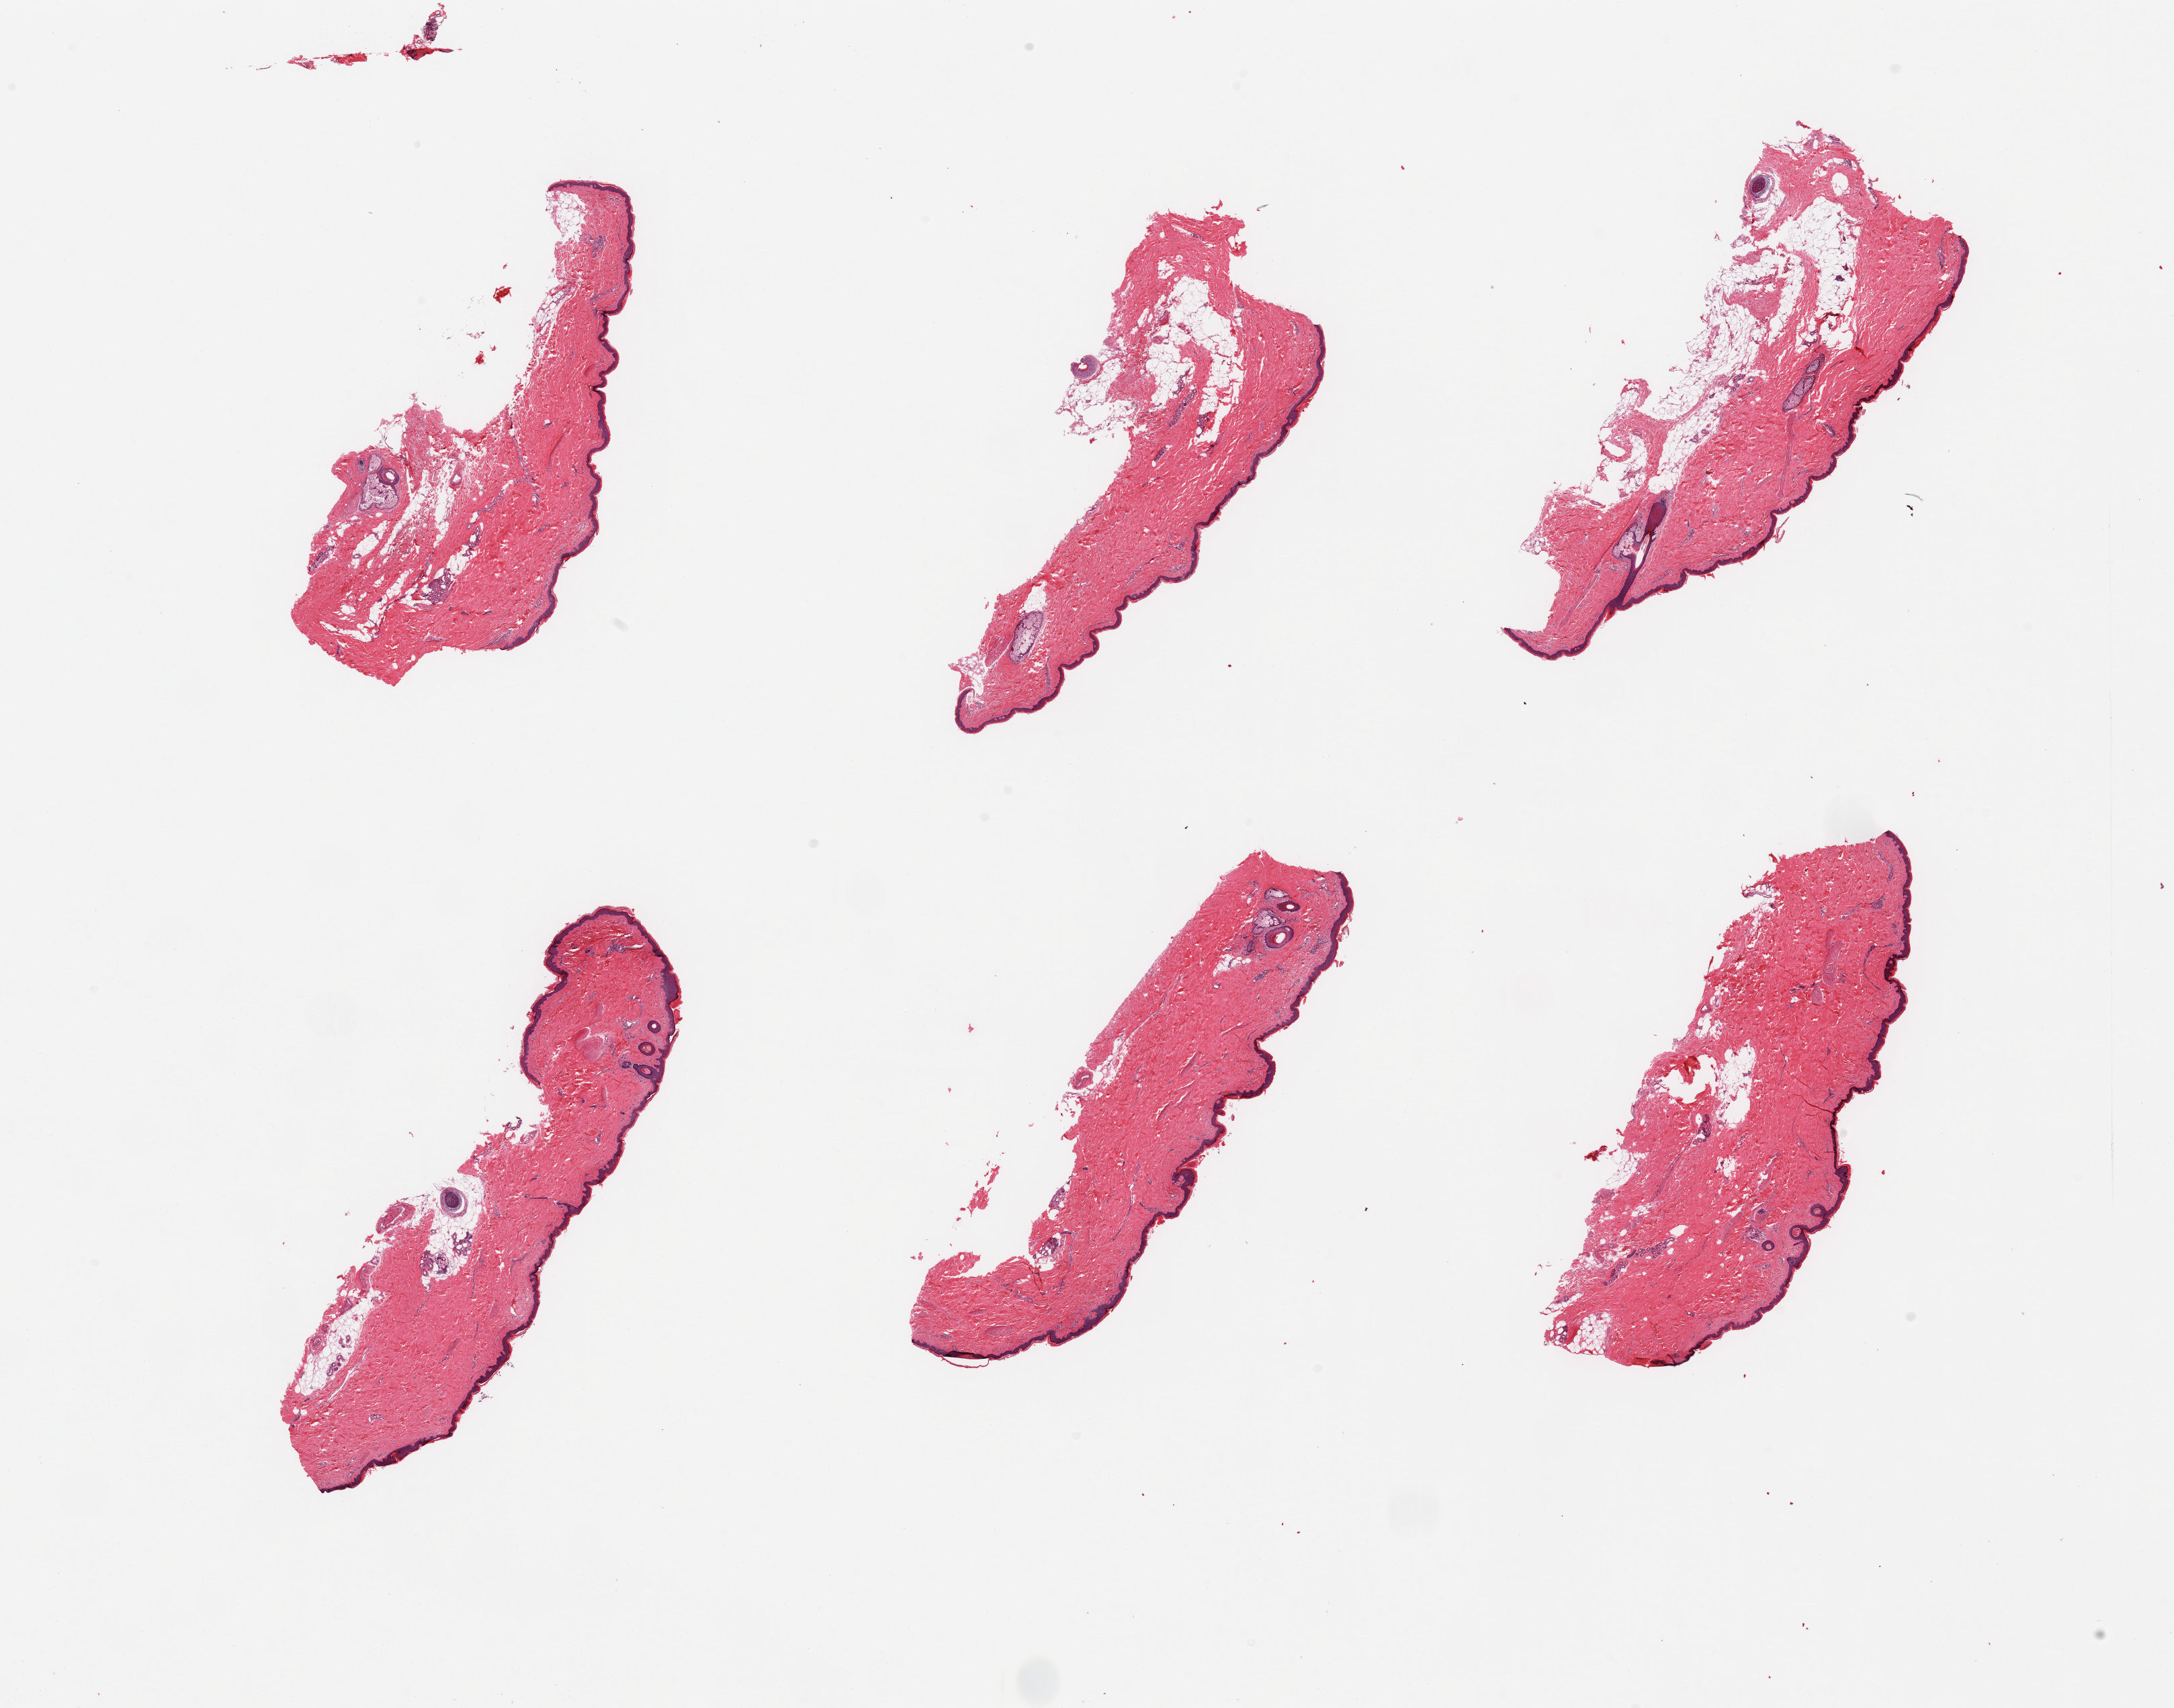
Haematoxylin and eosin whole-slide image, a low-resolution overview of the entire scanned area, about 25.6 x 20.1 mm (from a 20x scan). PAXgene-fixed, paraffin-embedded tissue. Sampled site (target tissue): skin of lower leg. Tissue donor sample. Male donor.
* pathologist's review note for this sample: 6 pieces trace dermal fat; squamous epithelium is ~40-50 microns